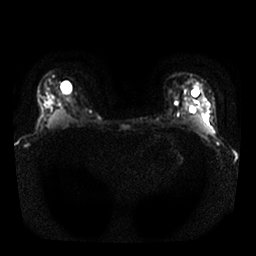
Breast MRI, one axial slice. Diffusion-weighted series; image 2 of 4 stored at this slice position (different b-values; order by instance number). 1.5 T. 4 mm slice thickness. 256 × 256 image matrix. Female patient.
Outlined on this slice (outlined manually by an expert reader):
- tumour on diffusion-weighted imaging: bounding box (x1, y1, x2, y2) in pixels: (198, 94, 210, 117)